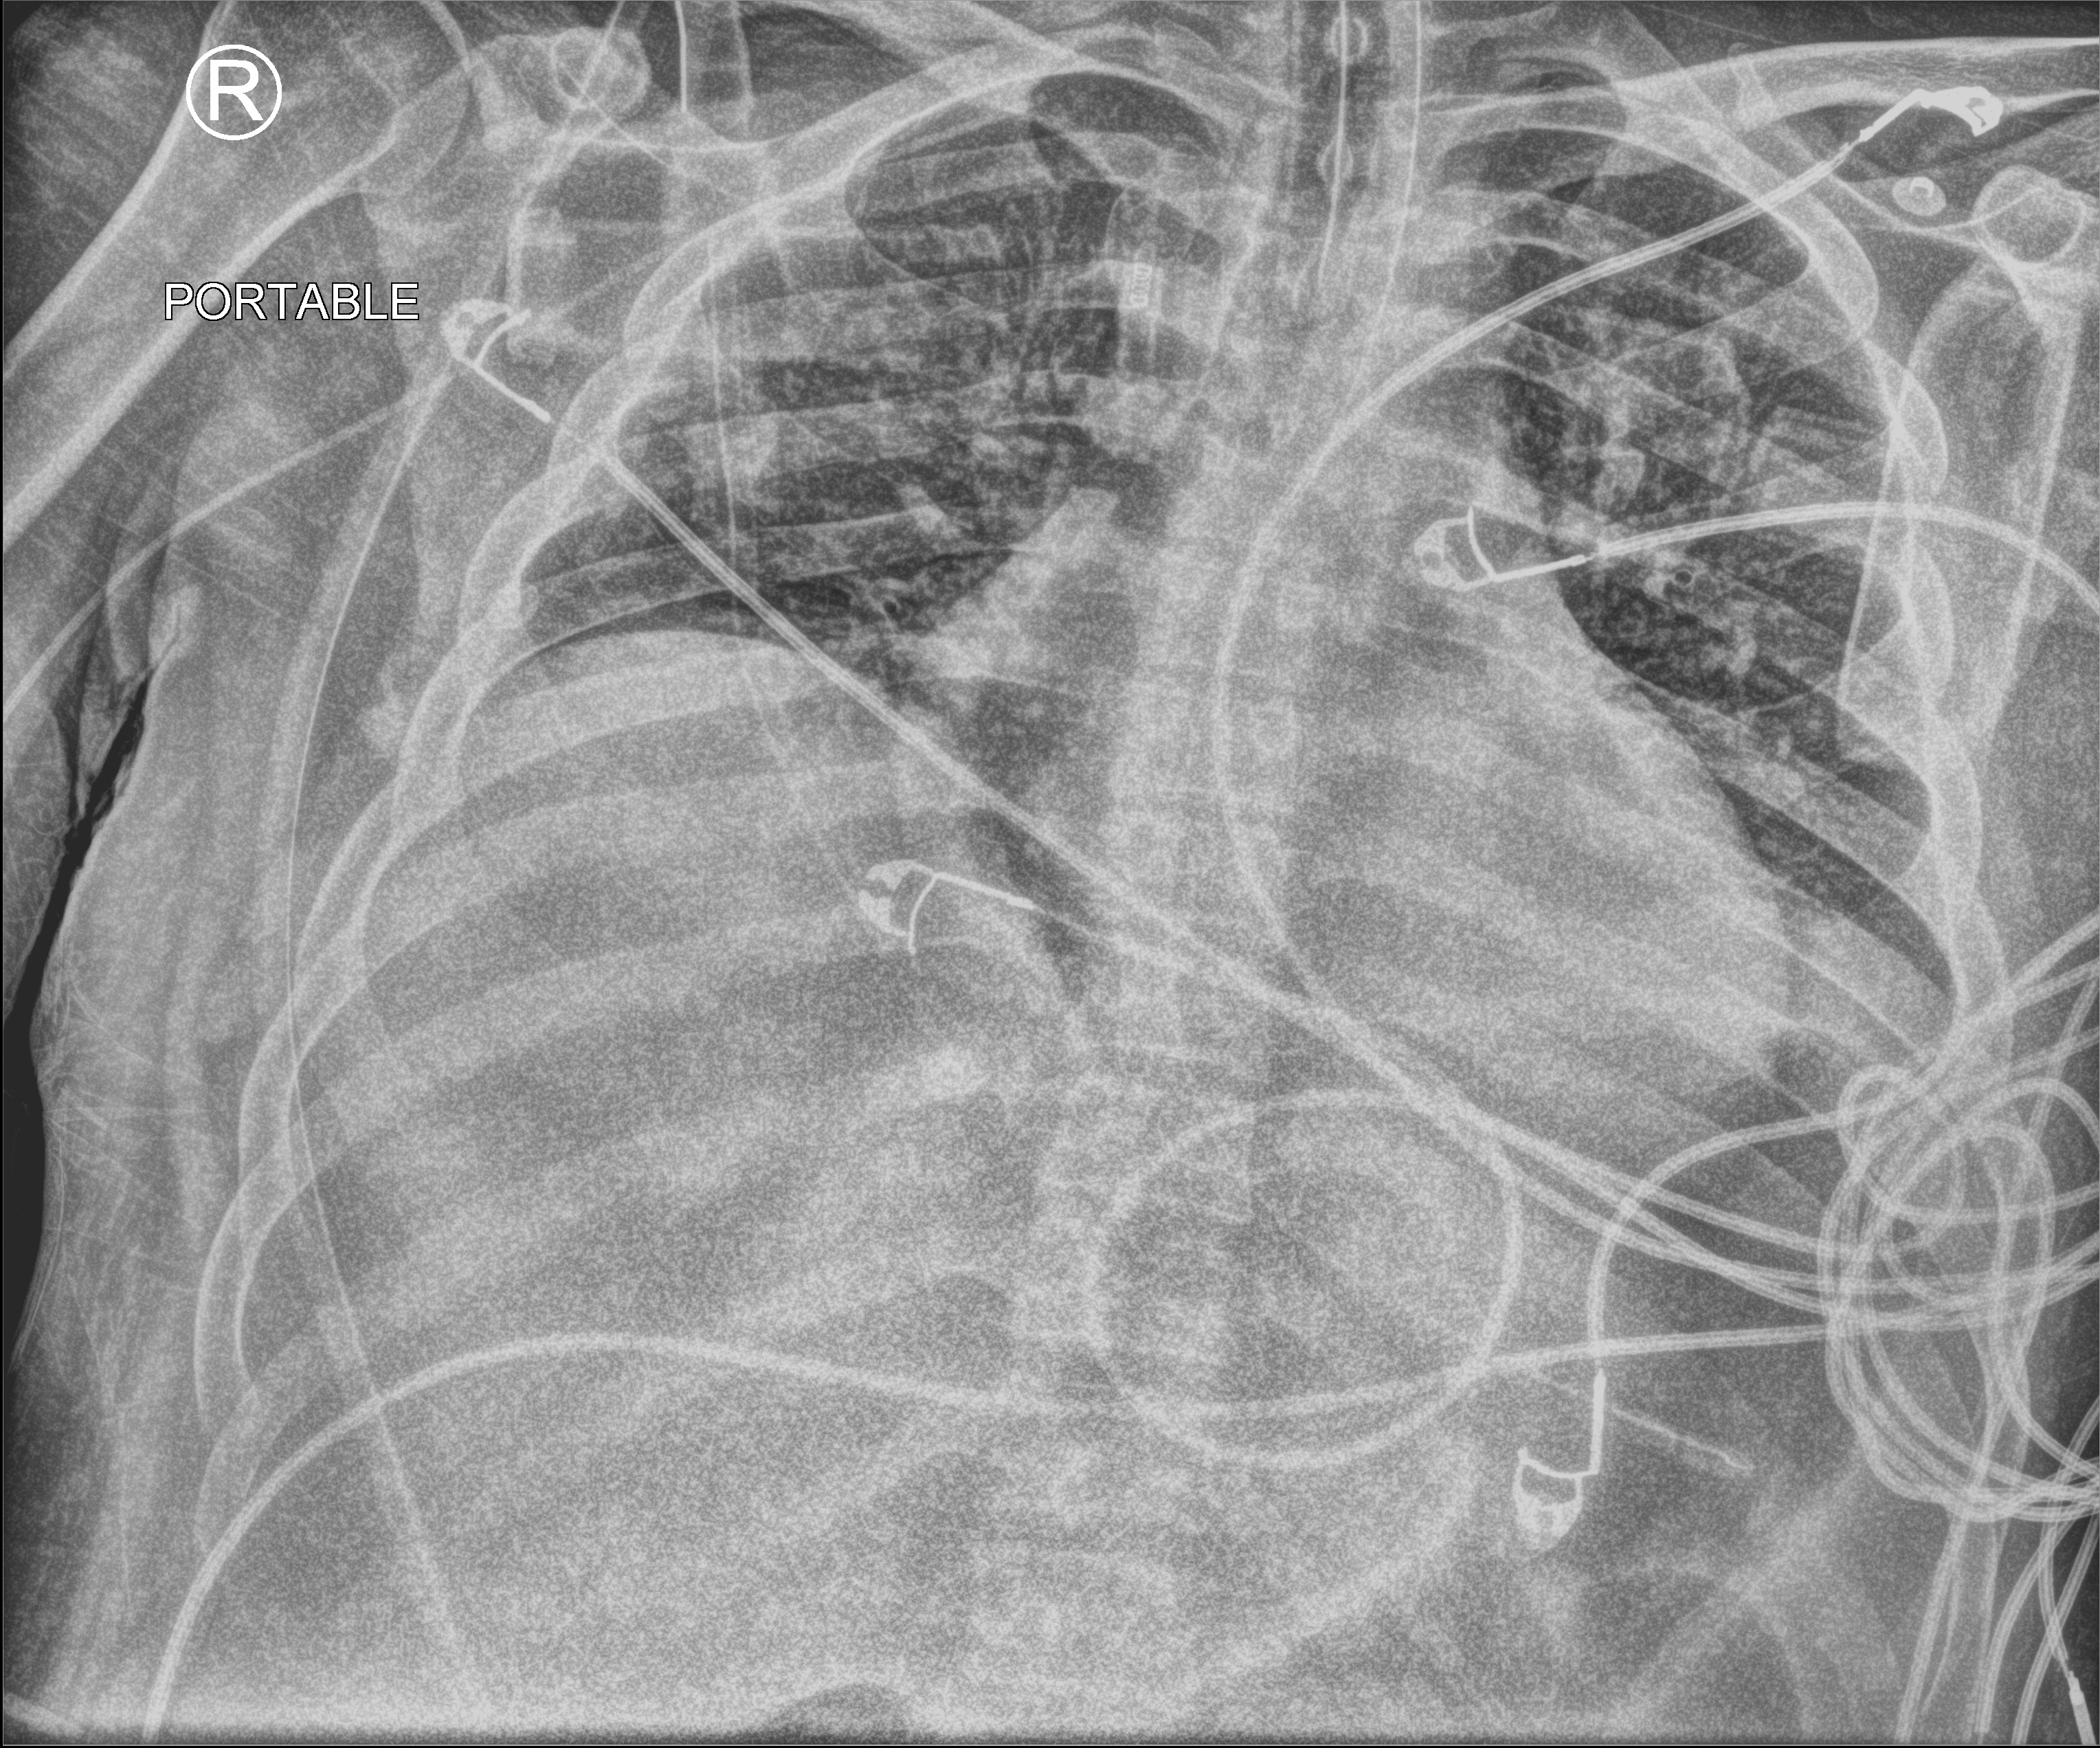
Bedside chest radiograph (computed radiography); anteroposterior (AP) projection. Male patient hospitalised with COVID-19, age 18–59 years.
Admission-level facts for this patient (not findings on this image; timing relative to this image not recorded): admitted to intensive care during this hospital stay: yes.